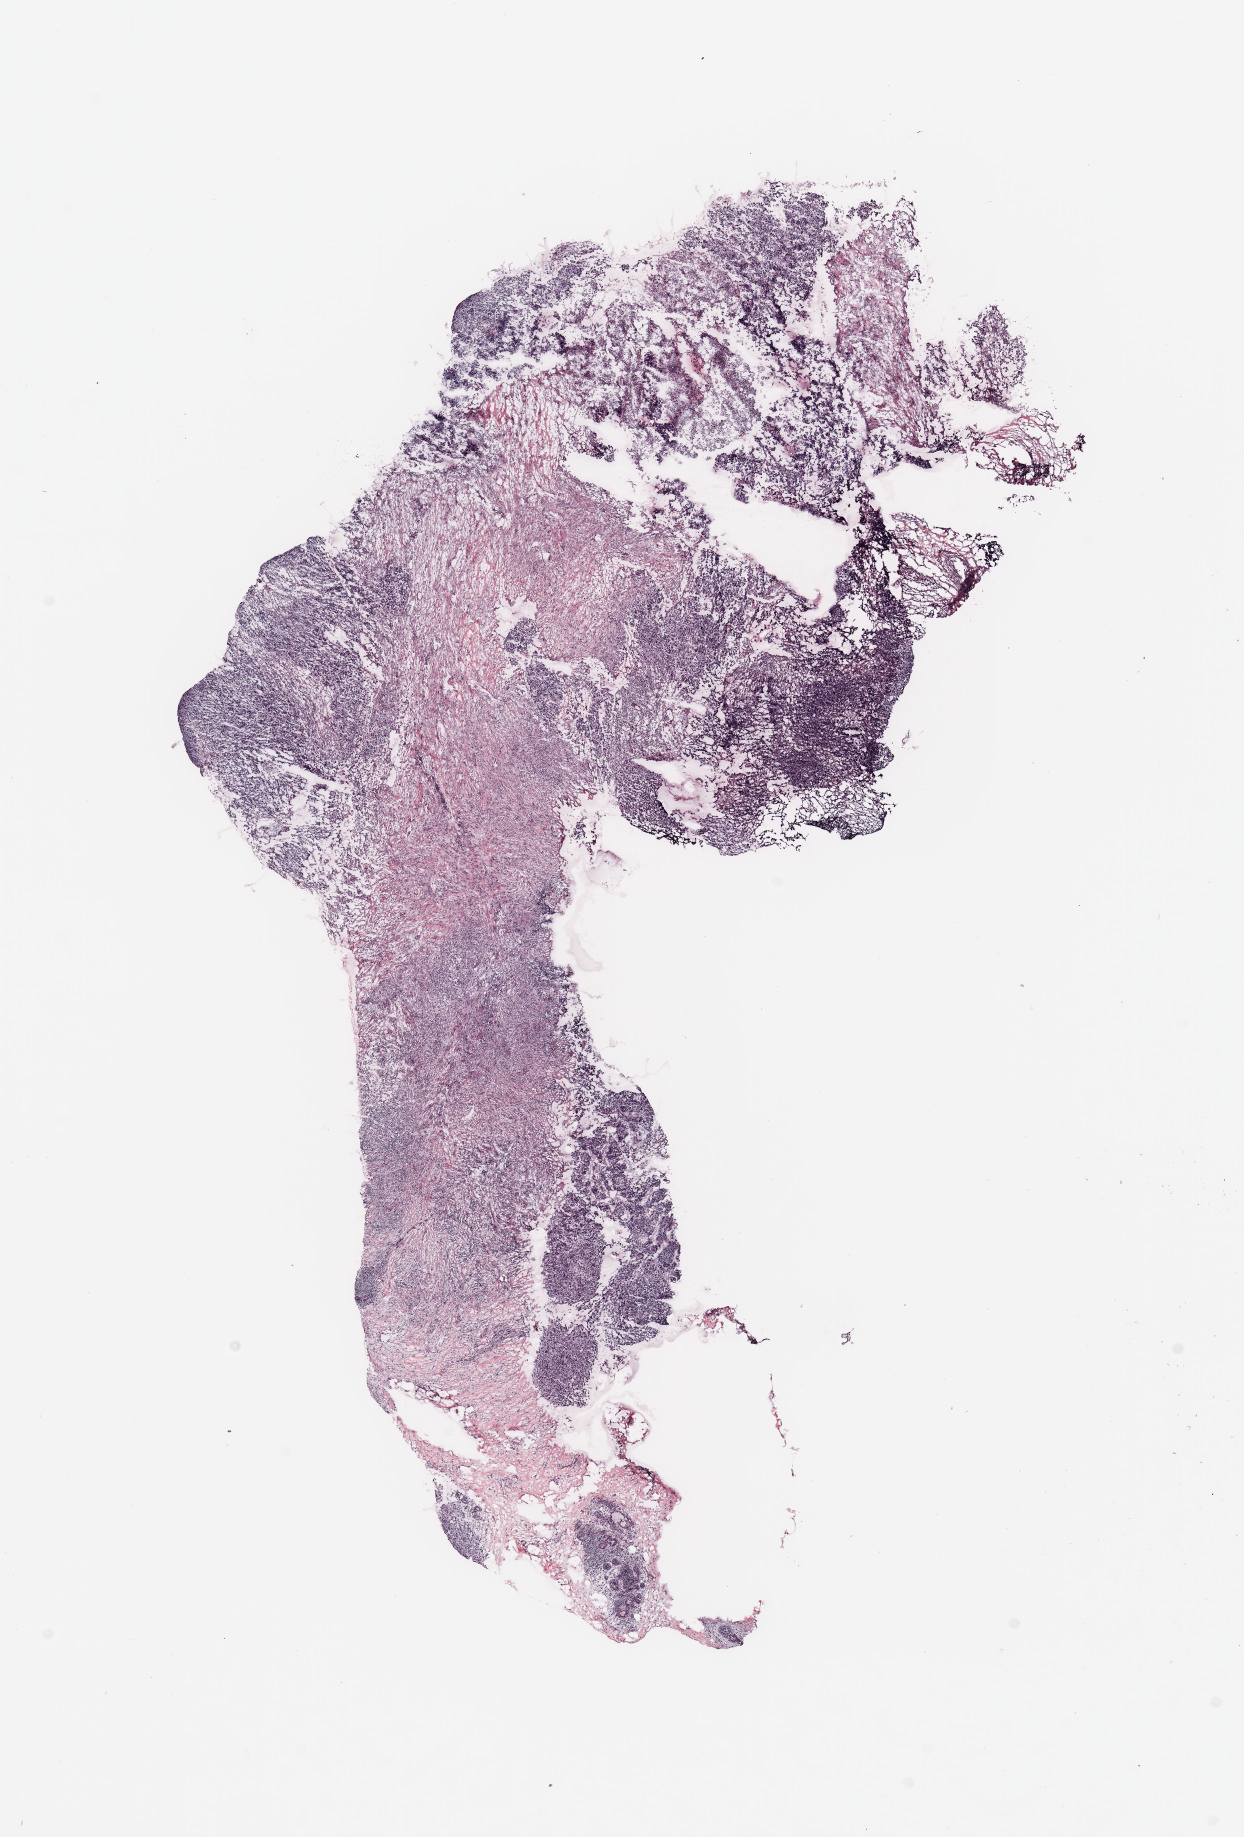
Digitized H&E tissue section (whole slide), whole scanned area (about 9.8 x 14.5 mm, slide scanned at 20x) shown as a low-resolution overview; tumour tissue sample, breast. Female, 66 y/o.
Histologic diagnosis: Infiltrating duct carcinoma, NOS. AJCC pathologic stage: IIIA.